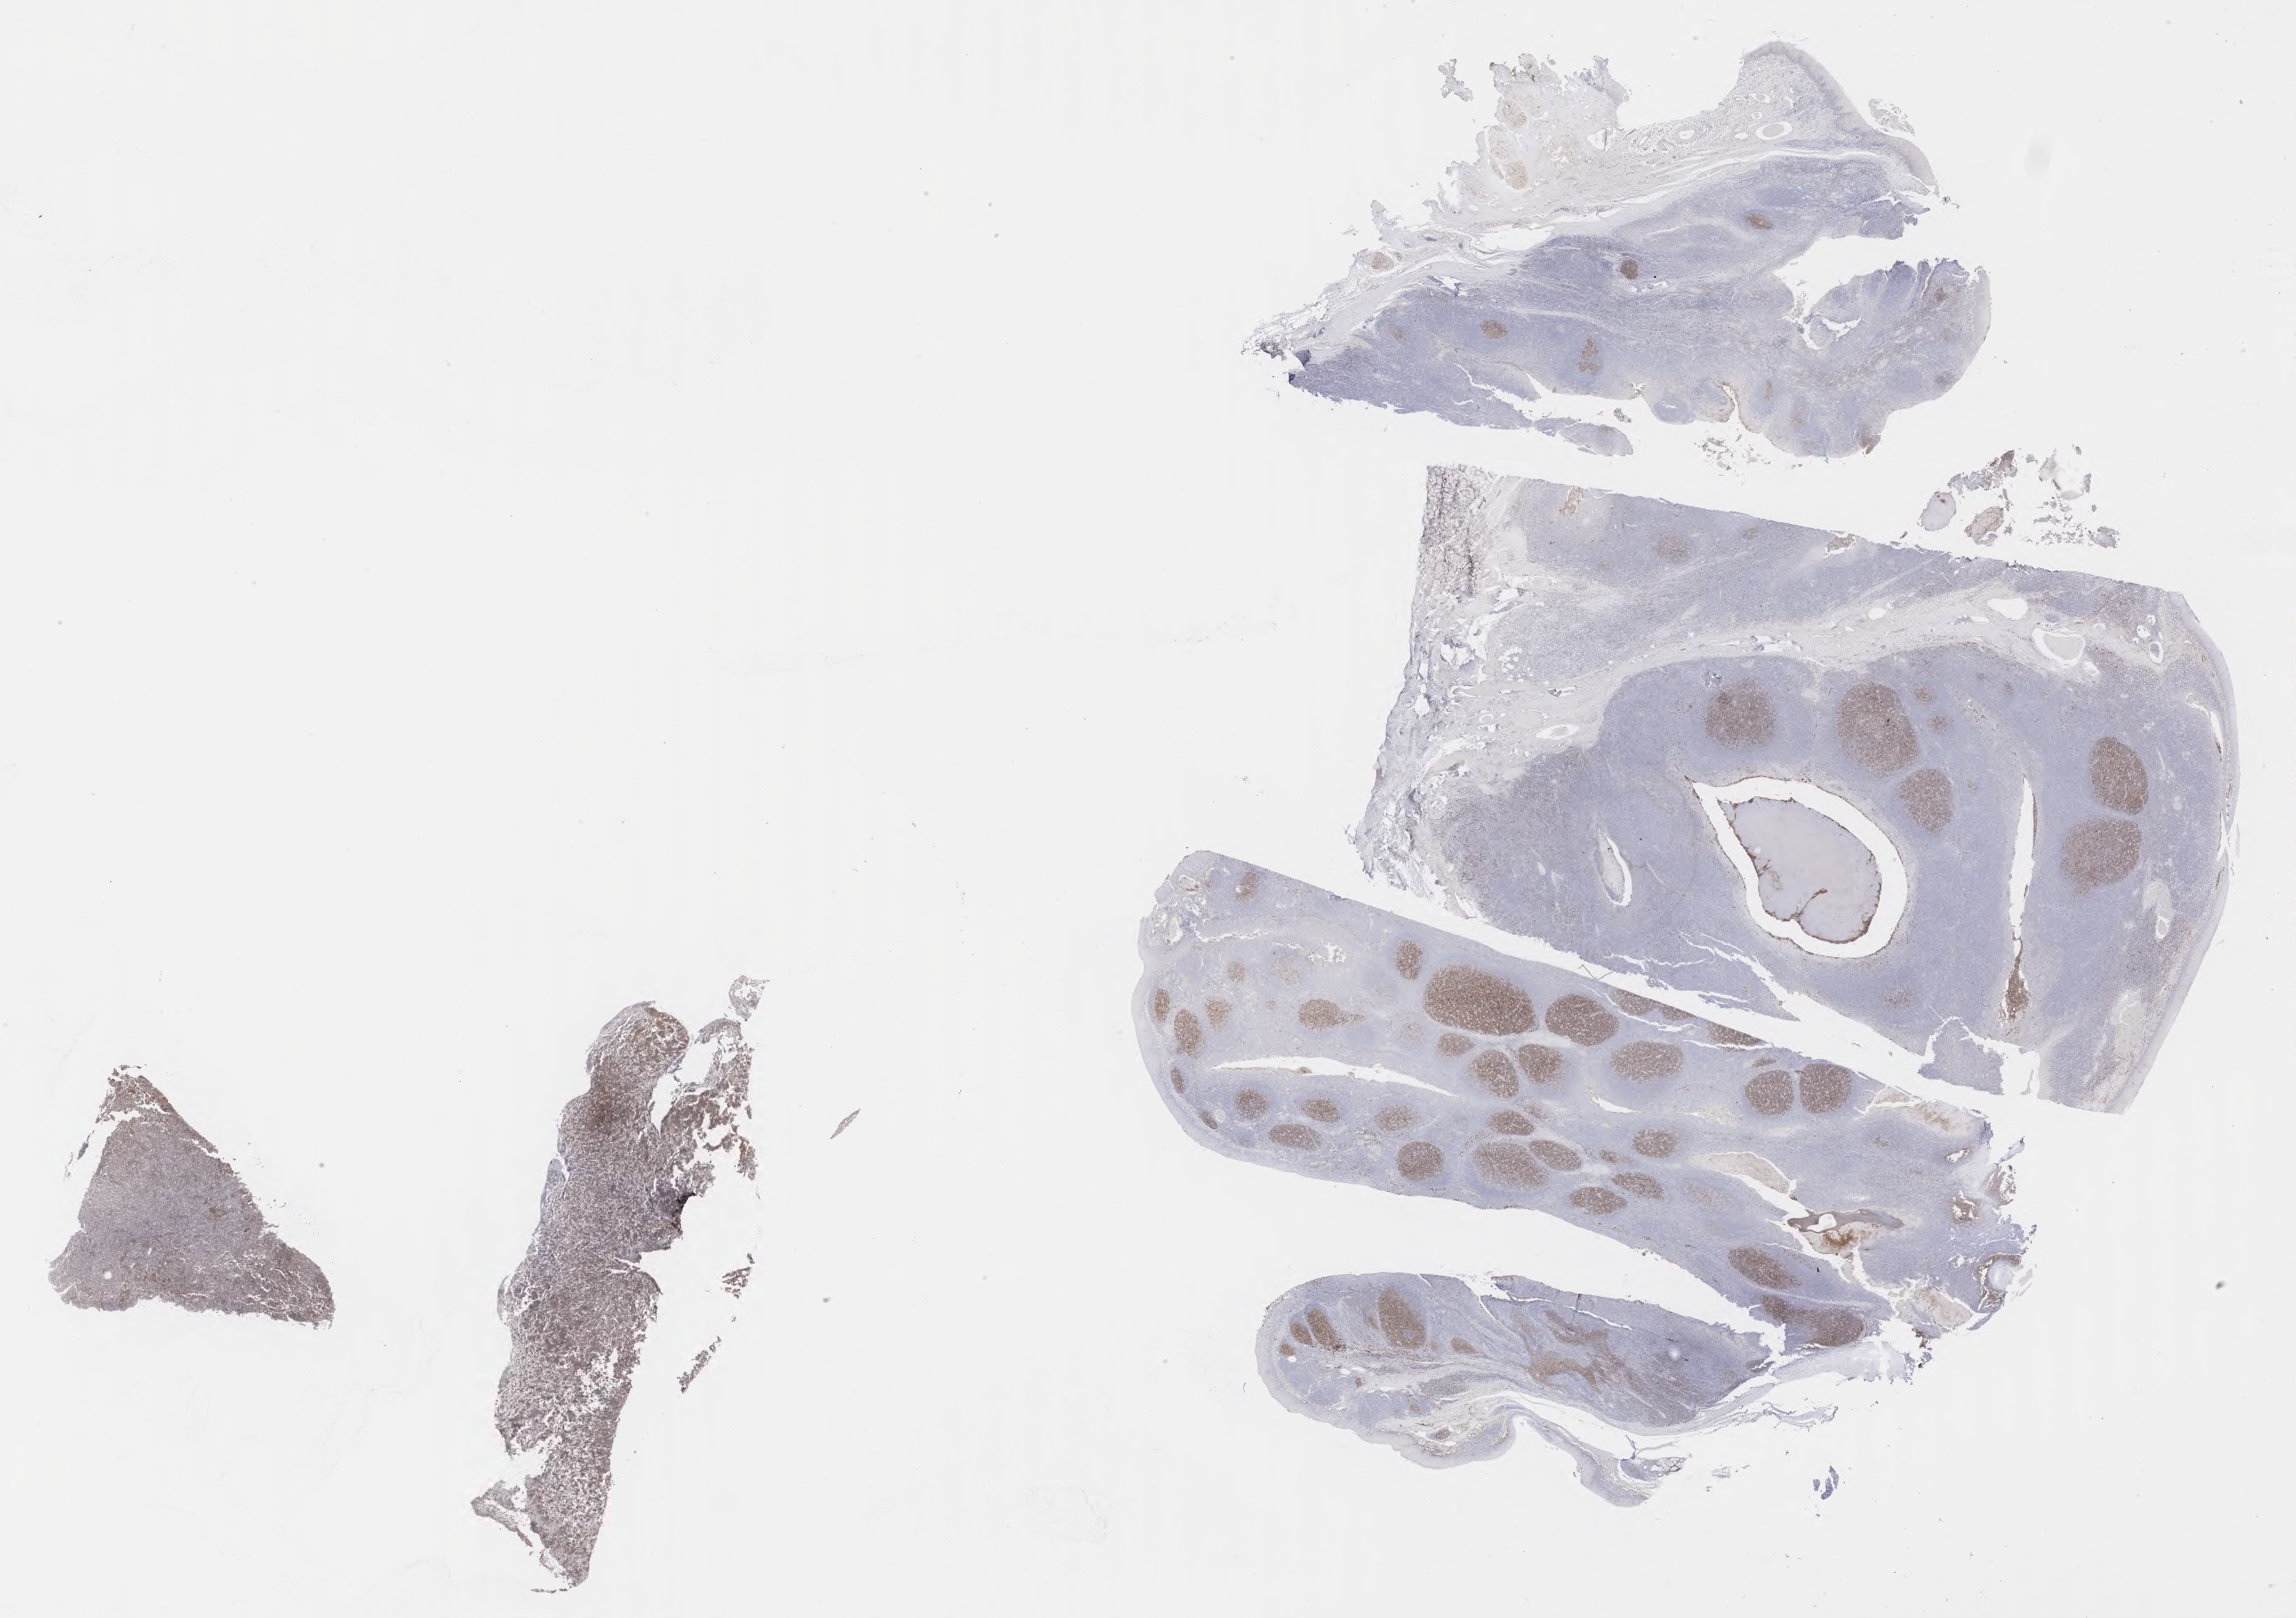
IHC for CD10, whole-slide image, low-resolution overview of the scanned area, about 29.2 x 20.6 mm; specimen: tumor tissue. Male, age 2 years at initial diagnosis.
- histologic diagnosis: Burkitt lymphoma, NOS